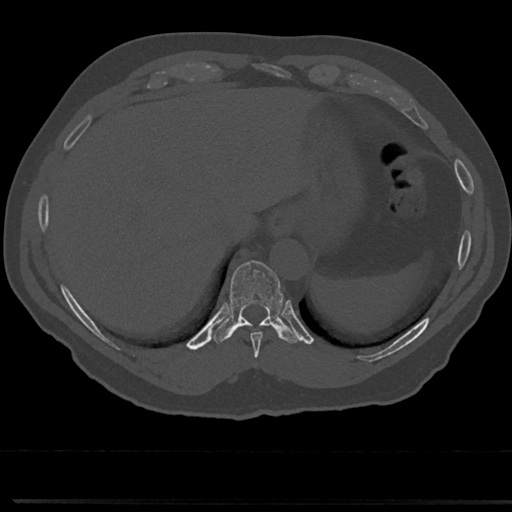
CT including the spine, one axial slice. Position 271 of 817 along the scan axis. Bone window (W 1800 / L 400 HU). 0.5 mm slice thickness. 512 × 512 image matrix, field of view 355 × 355 mm. Male patient, age 61 years. From the clinical record (not read from this slice): primary cancer: prostate.
Outlined on this slice (semi-automatic segmentation, software-assisted and operator-edited):
- T10 vertebra: box from (x=229, y=261) to (x=282, y=324) px
- T9 vertebra: (x=235, y=322)–(x=281, y=352)